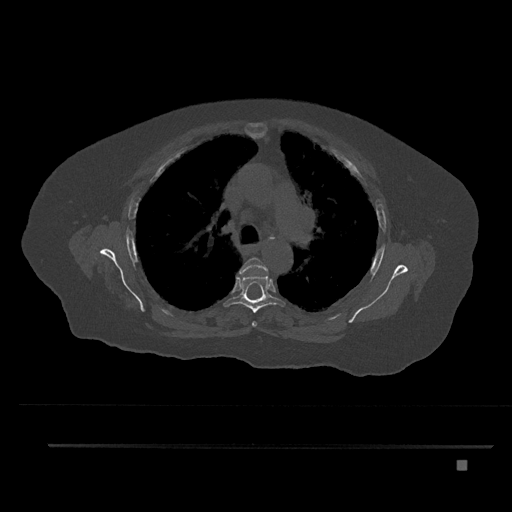
CT including the spine, one axial slice. Slice 574 of 797 in the series (ordered by position). Reconstruction kernel Br40s/3. Bone window (W 1800 / L 400 HU). 512 × 512 image matrix, field of view 437 × 437 mm. Female patient, age 76 years. From the clinical record (not read from this slice): primary cancer: lung.
Outlined on this slice (semi-automatically segmented with operator editing):
- T4 vertebra: bounding box [x1, y1, x2, y2] px = [239, 257, 268, 327]
- T5 vertebra: [223, 275, 285, 313]